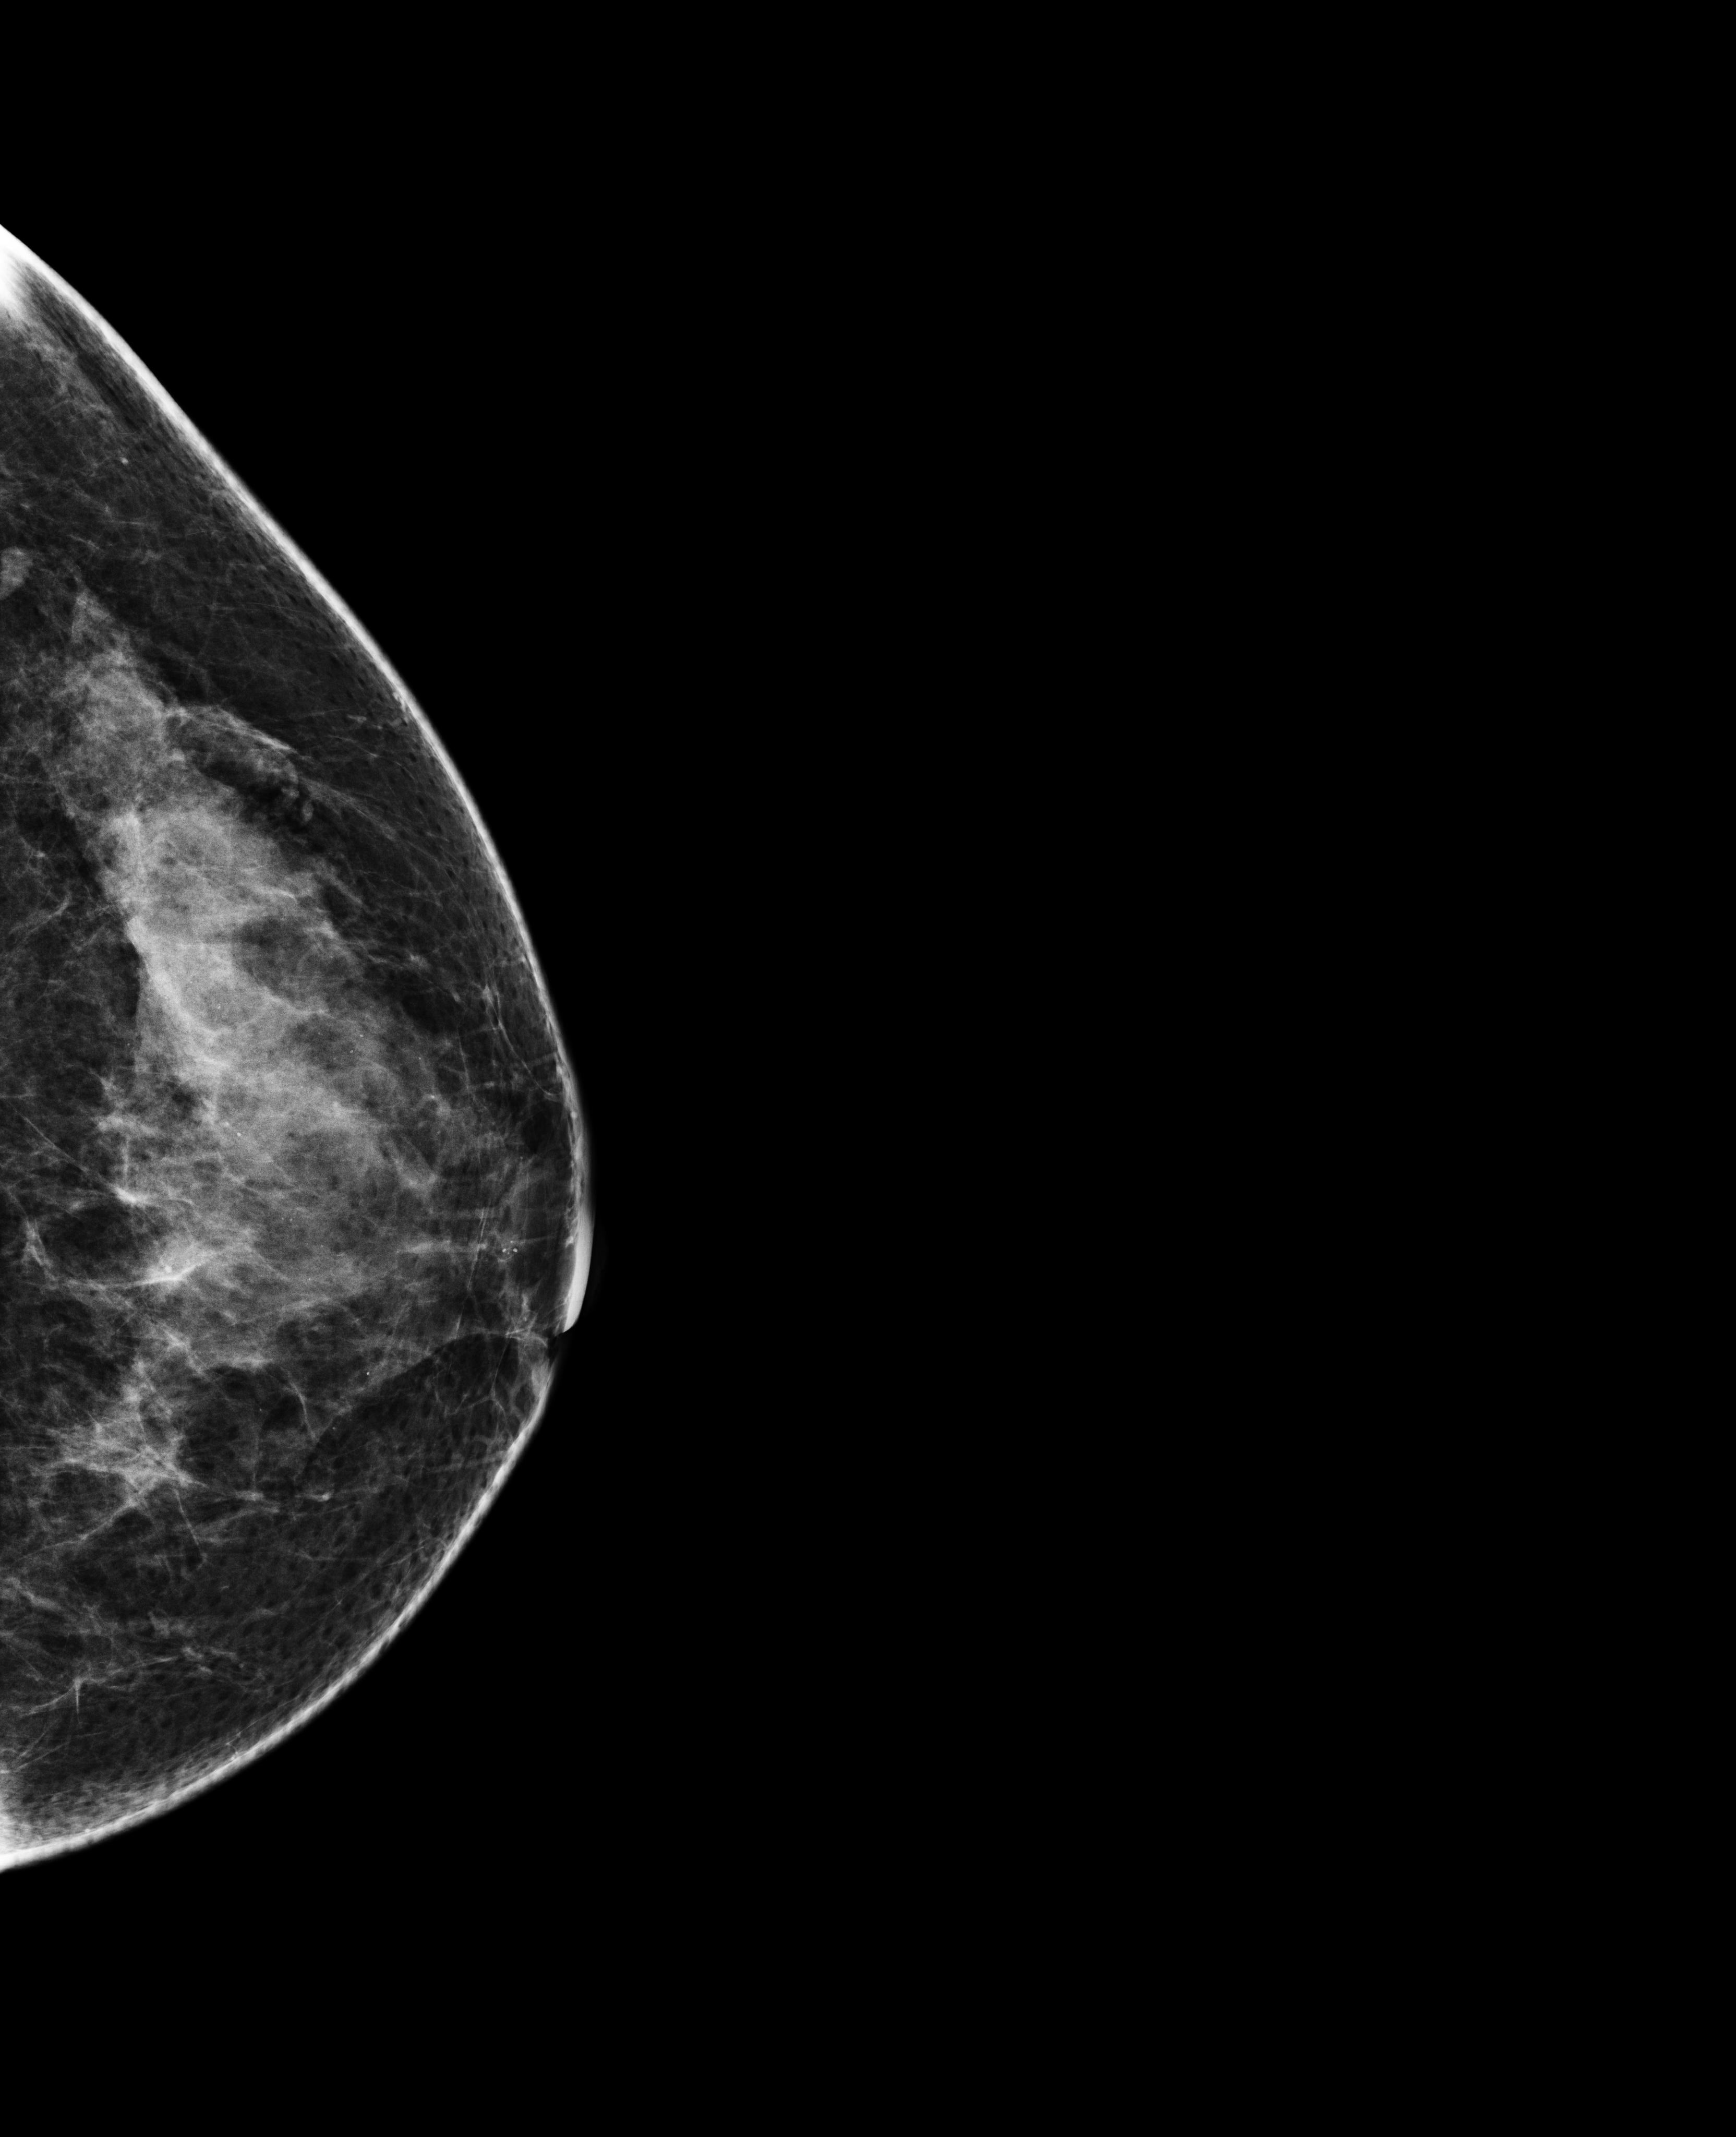
Screening examination. Female patient, age 49 years.
Image type: full-field digital mammogram. Breast: left. Projection: craniocaudal (CC) view.